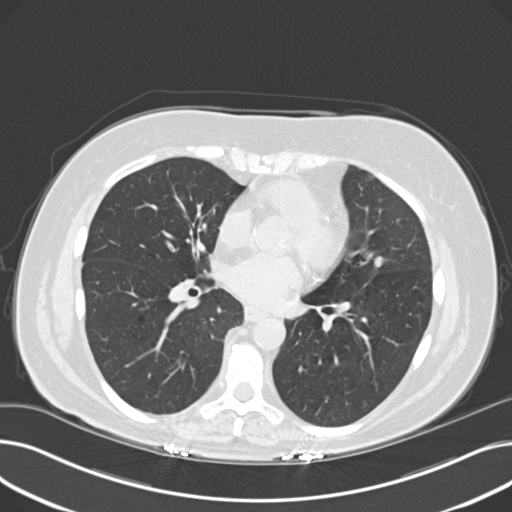
Low-dose screening chest CT, axial slice, third screening round (two years after baseline), lung window (W 1500 / L -600 HU), 2 mm slice thickness. Female participant, aged 60 years at enrolment.
Expert reader's lesion annotation, bounding box <362,251,397,282> (left, top, right, bottom; pixels). The screening reader recorded 8 non-calcified nodules or masses ≥4 mm on this exam (right upper lobe, lingula, lingula, right middle lobe, right lower lobe, left lower lobe, left lower lobe, left lower lobe); which of them this box marks is not recorded. Official screen result: positive, other. Lung cancer was diagnosed 176 days after this screen: non-small cell carcinoma, left upper lobe, poorly differentiated (G3), stage IB (AJCC 6th edition), 7 mm at pathology.